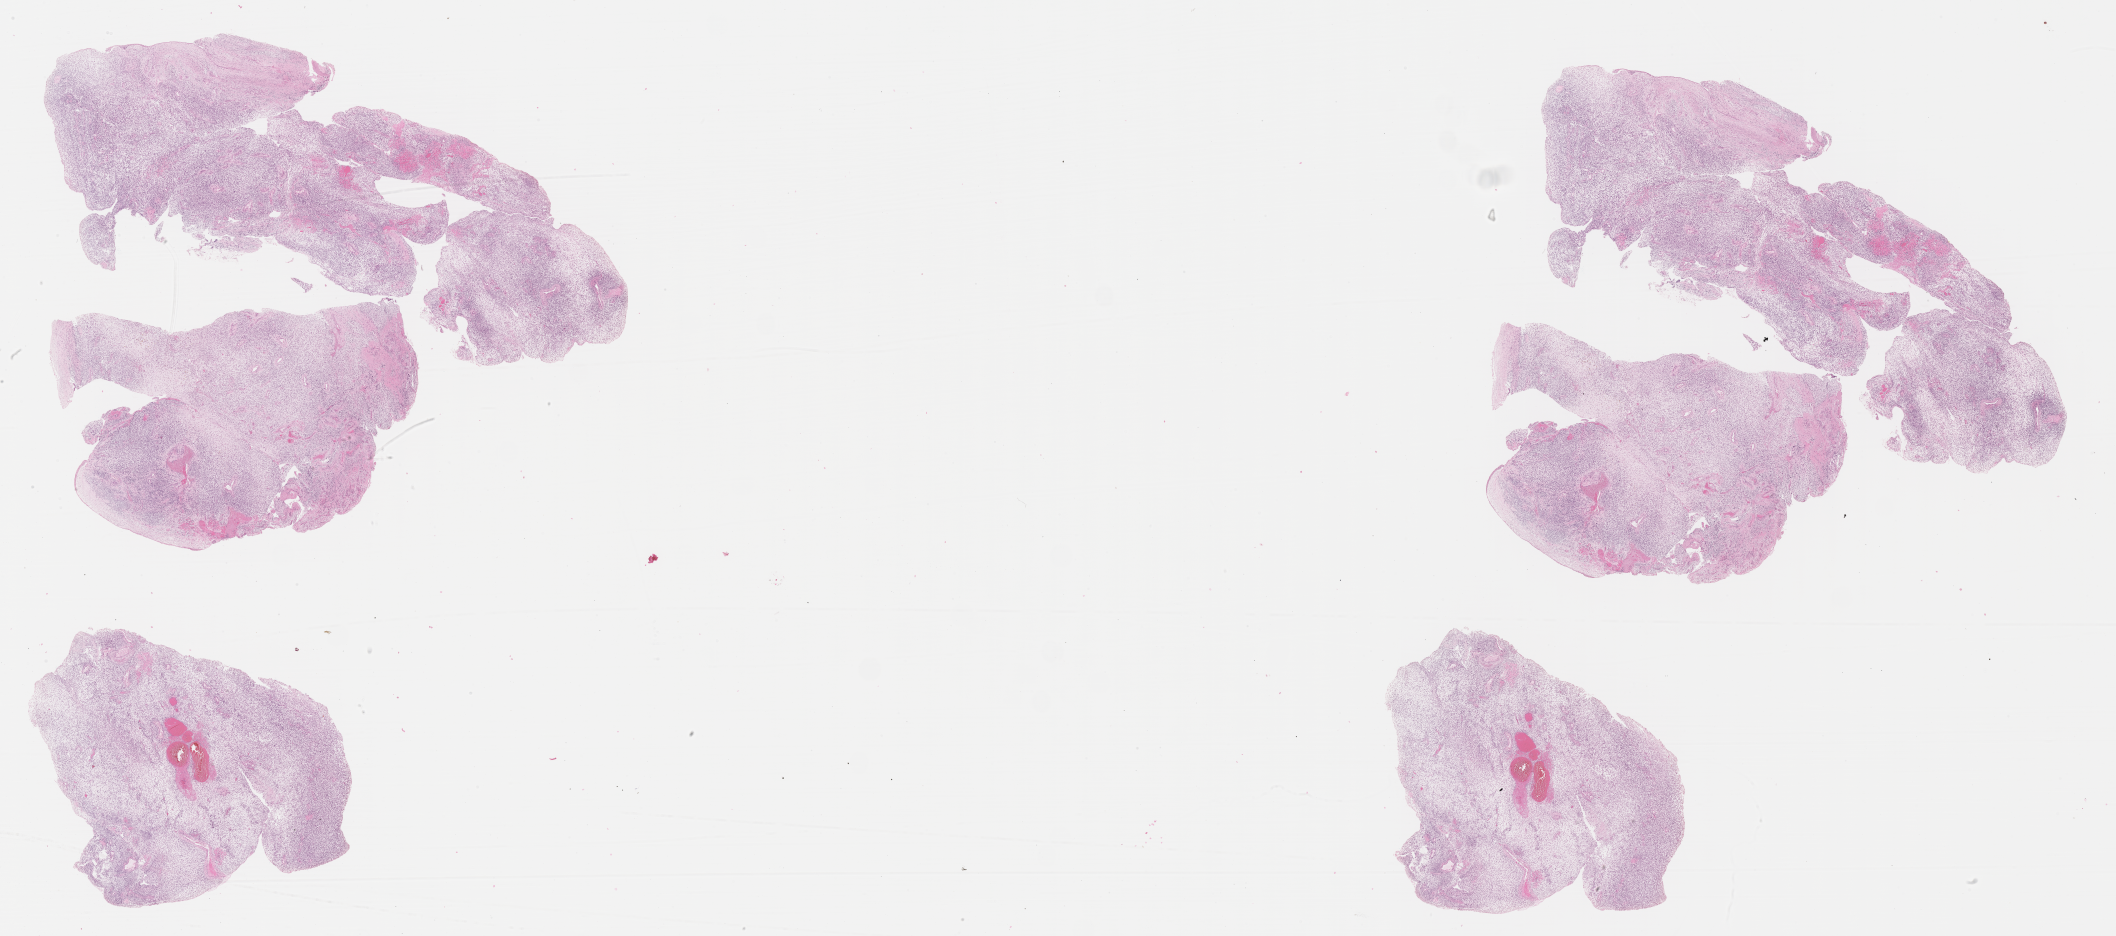
Whole-slide image, hematoxylin and eosin (H&E) stain of tumor tissue — a low-resolution overview of the entire scanned area, about 34.2 x 15.1 mm. Formalin-fixed paraffin-embedded section. Female patient, age at diagnosis 5.8 years.
- stage (as recorded): 3
- metastatic status at presentation (as recorded): non-metastatic
- diagnosis: rhabdomyosarcoma; histological classification: embryonal rhabdomyosarcoma